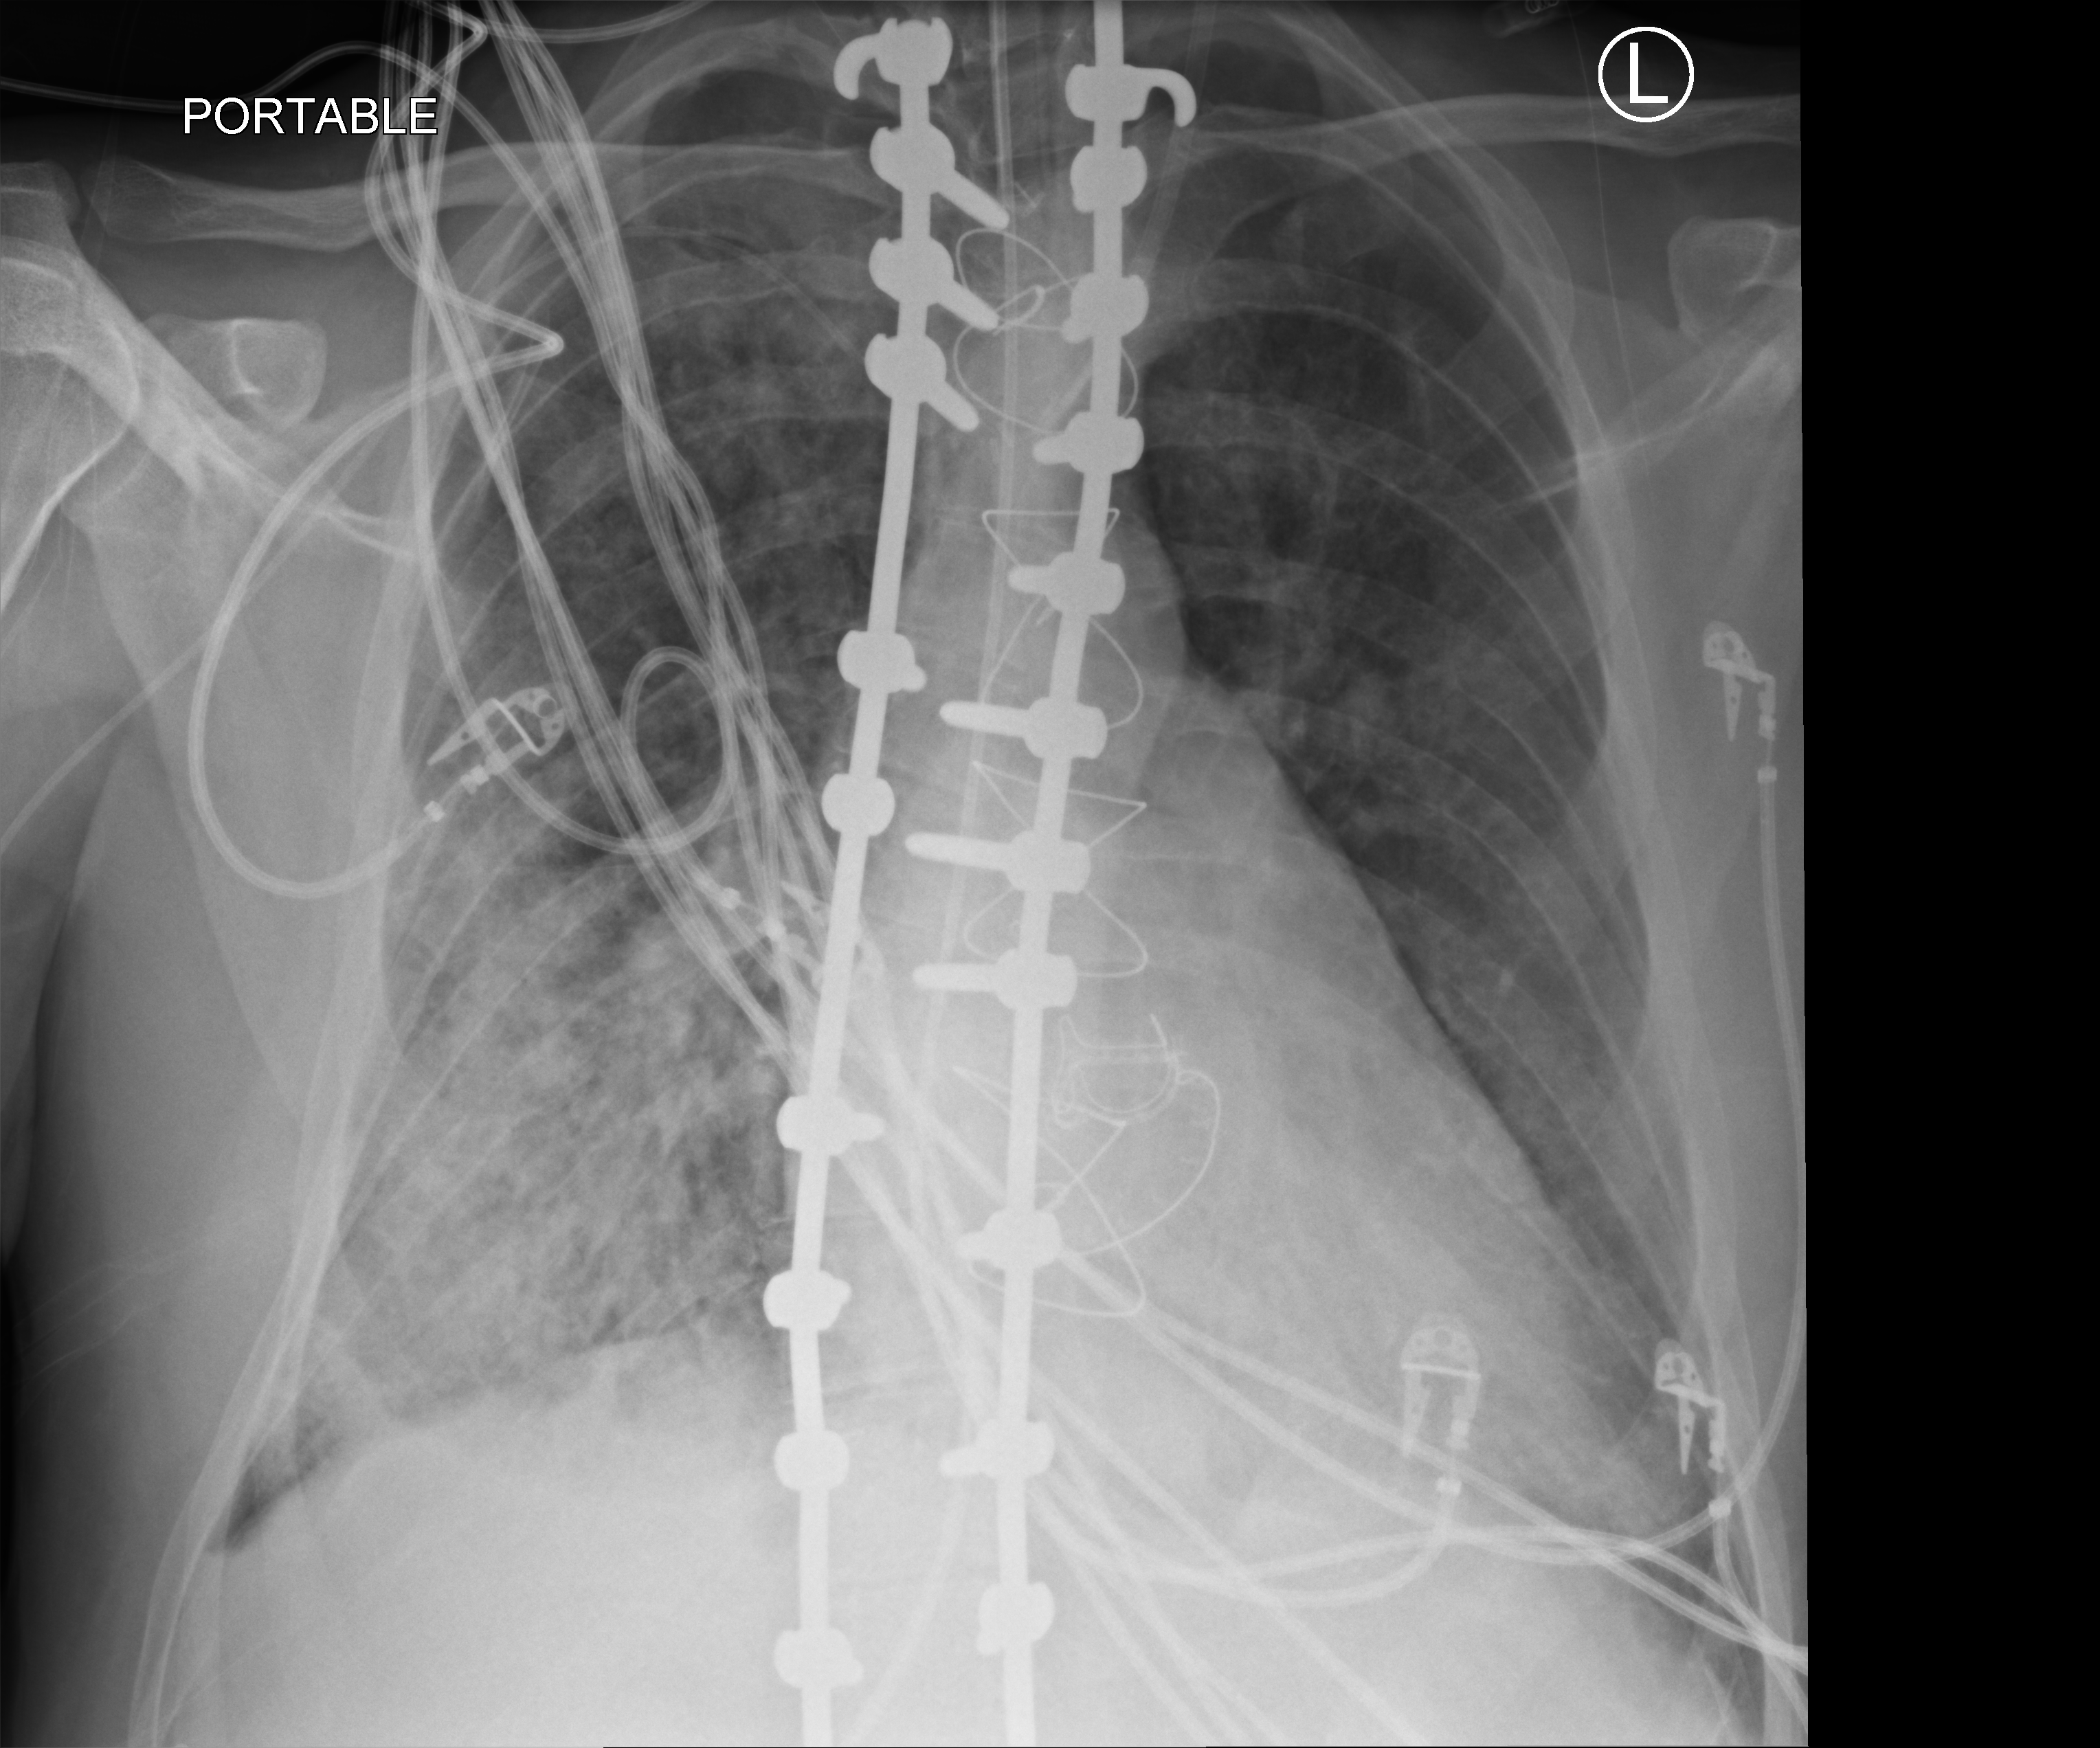
Bedside chest radiograph (computed radiography). Patient hospitalised with COVID-19, aged 18–59 years.
Admission-level facts for this patient (not findings on this image; timing relative to this image not recorded):
- mechanically ventilated during this hospital stay: yes
- admitted to intensive care during this hospital stay: yes